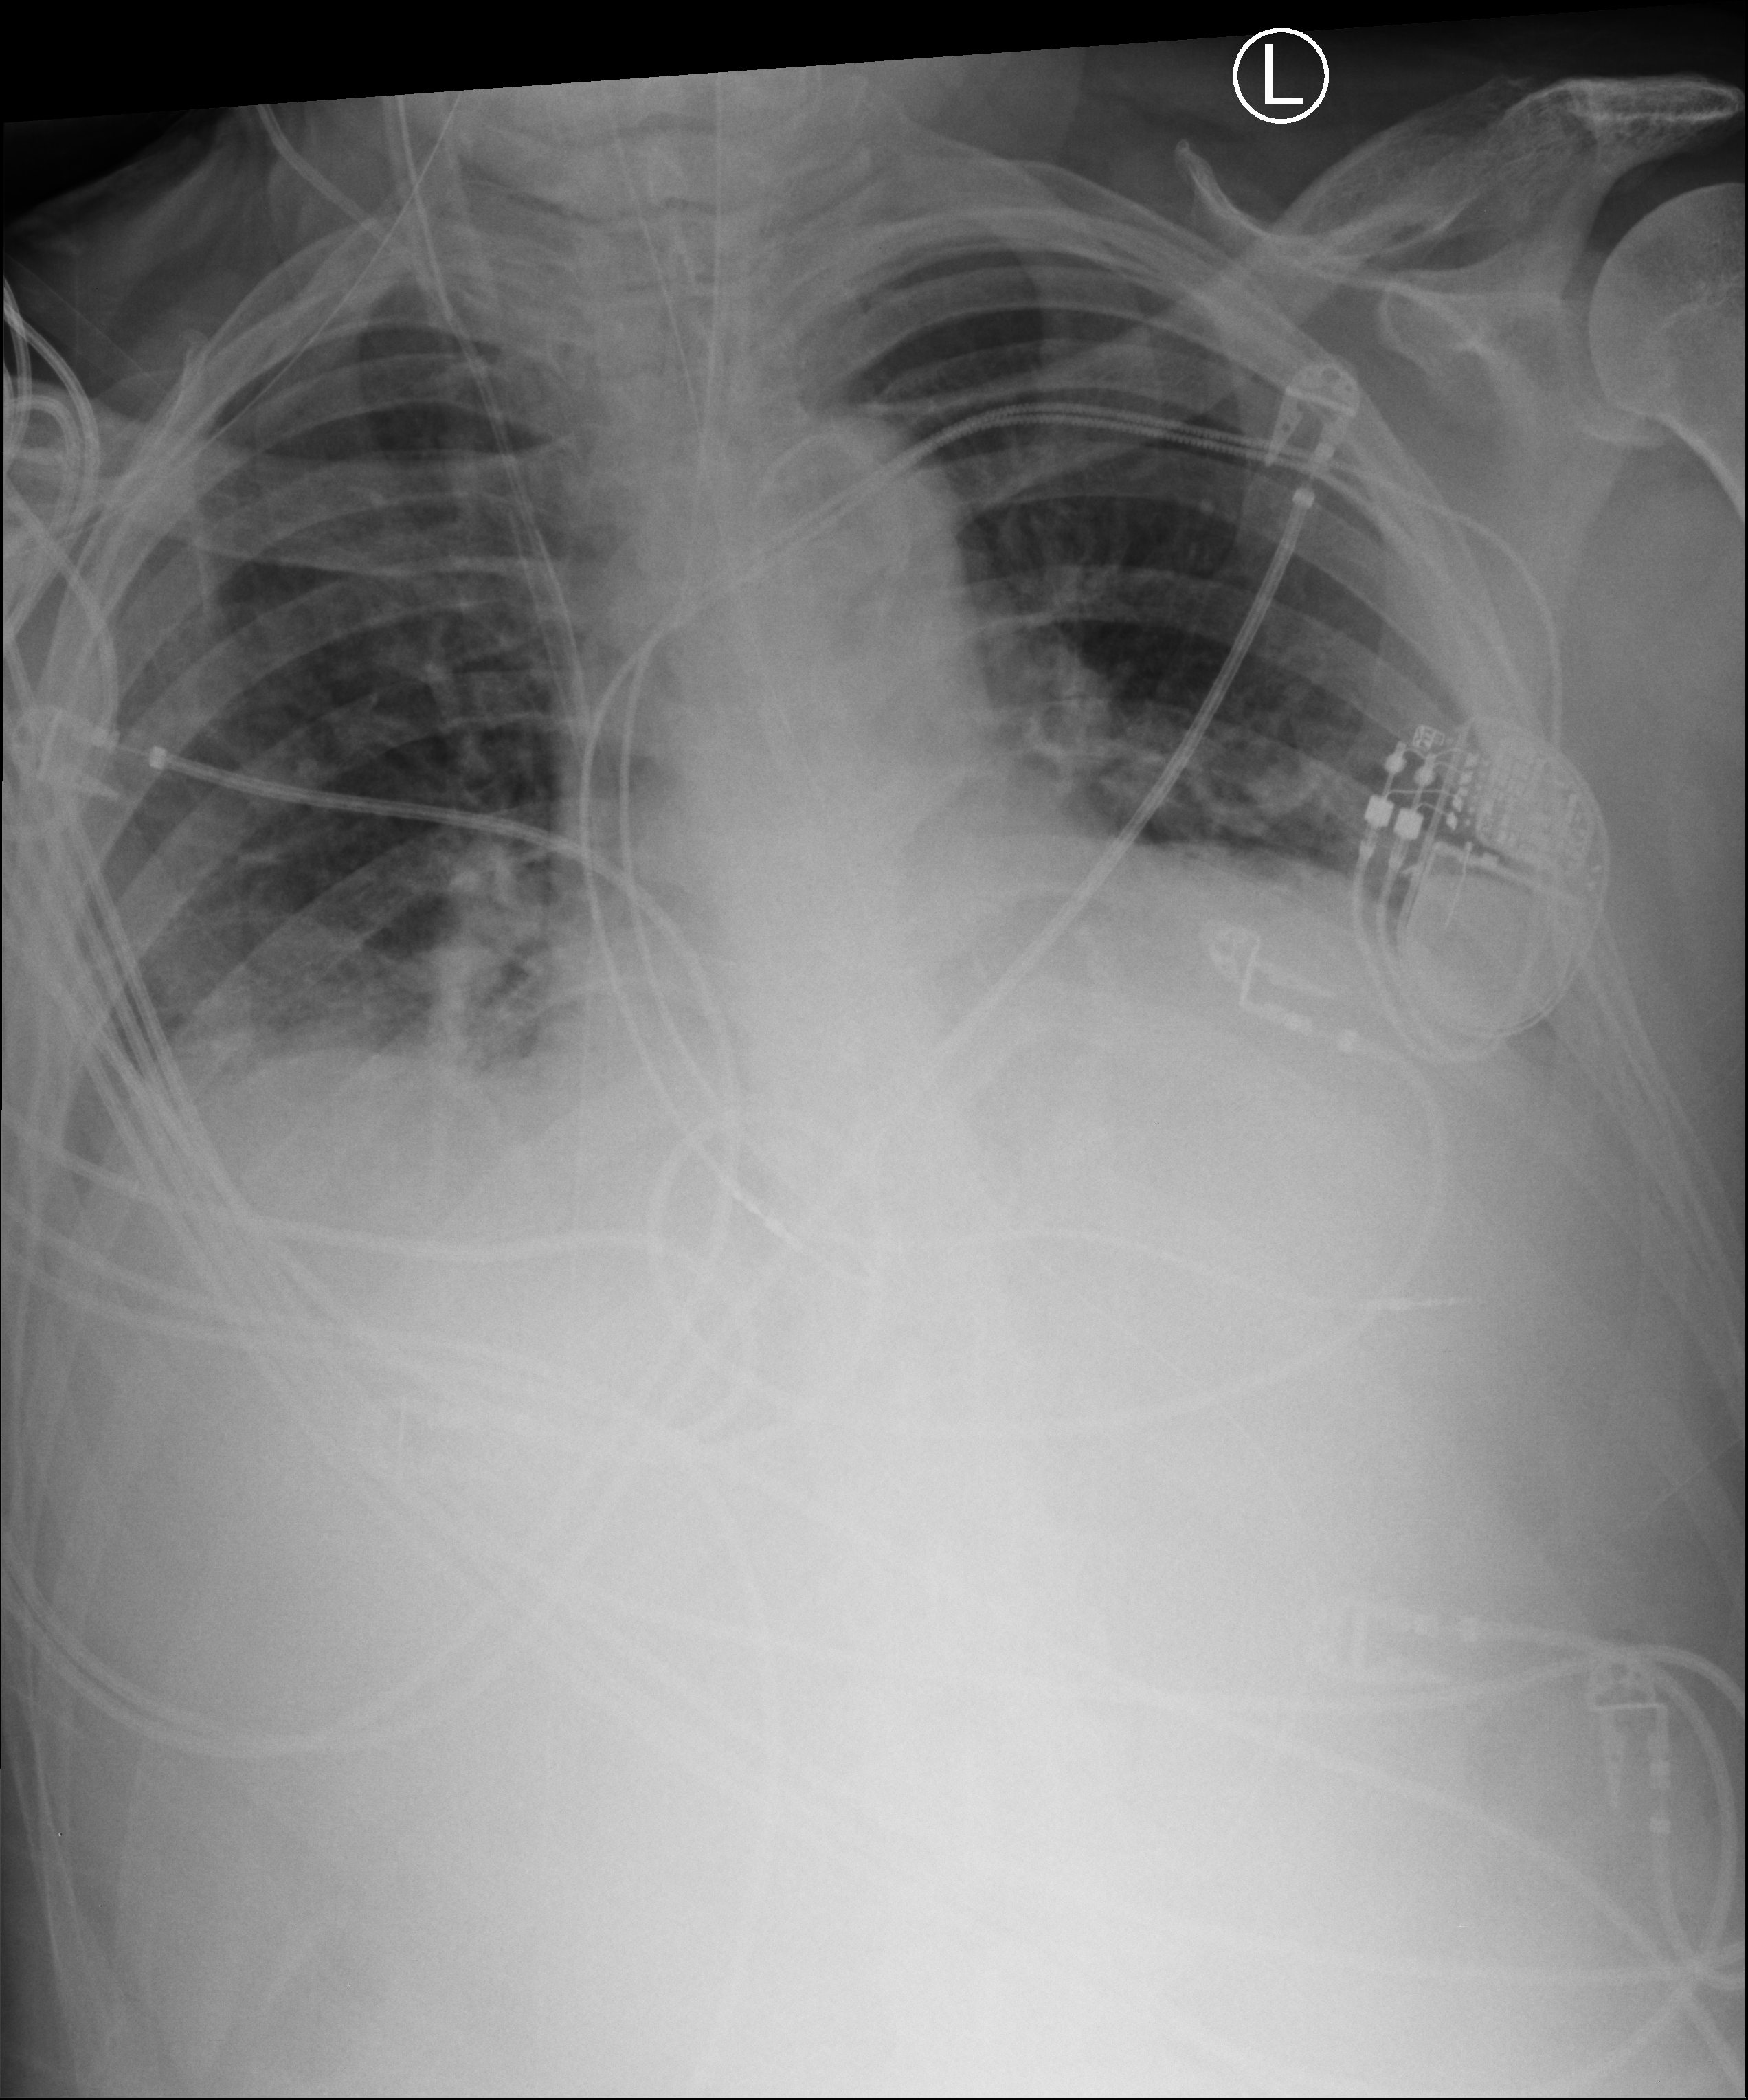
Bedside chest radiograph (computed radiography); anteroposterior (AP) projection. Male patient hospitalised with COVID-19, age 60–74 years.
Hospital-stay facts (about this admission, not read from this image; timing relative to this image not recorded): admitted to intensive care during this hospital stay: yes.